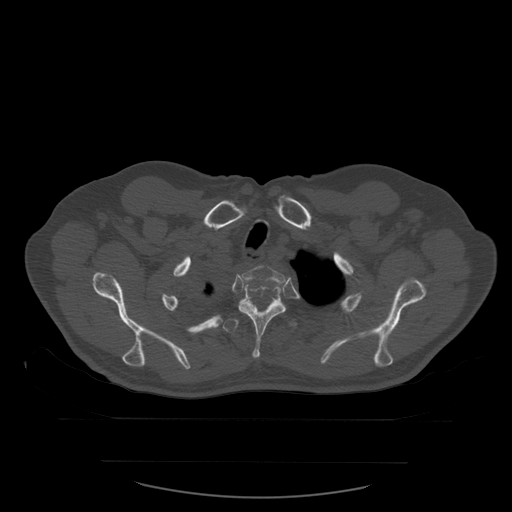
CT including the spine, one axial slice; slice 458 of 590 in the series (ordered by position); bone window (W 1800 / L 400 HU); 512 × 512 image matrix. Patient age 71 years. Case-level facts recorded for this patient, not image findings: primary cancer: lung.
Outlined on this slice (semi-automatic segmentation, software-assisted and operator-edited):
- T2 vertebra: bounding box <242,266,285,283> (left, top, right, bottom; pixels)
- T3 vertebra: <238,286,286,359>
- T4 vertebra: <223,299,298,333>